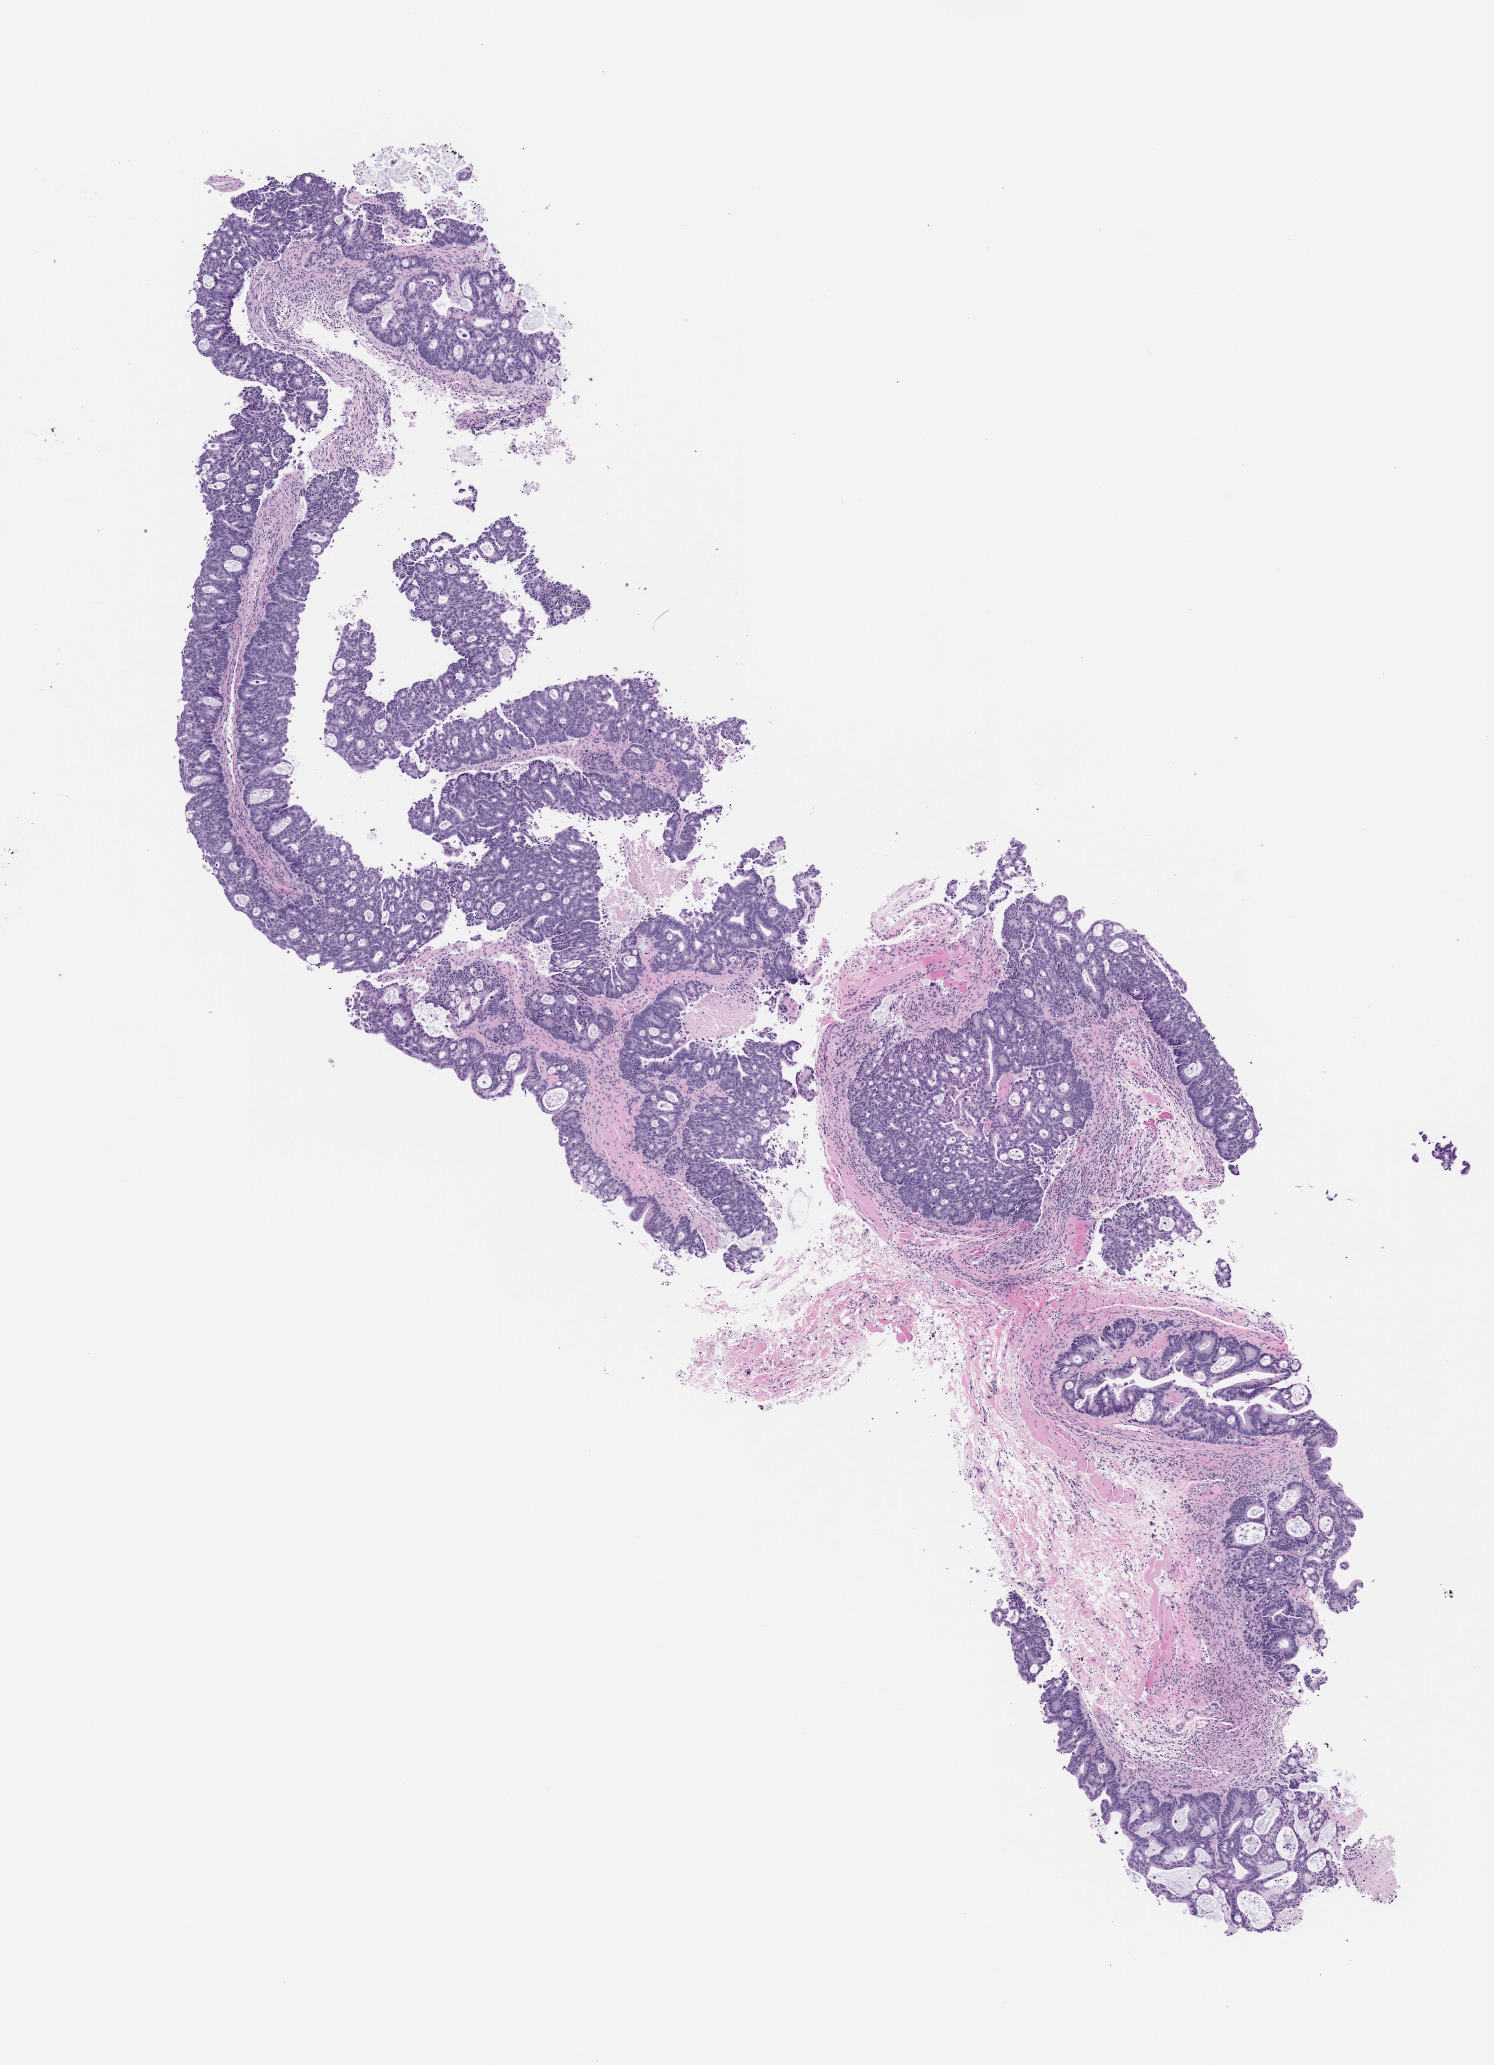
H&E whole-slide image of a patient-derived xenograft (PDX) tumor grown in a mouse, passage 1 — a low-resolution overview of the entire scanned area, about 6.0 x 8.3 mm, formalin-fixed paraffin-embedded section, originating tumor site category: colon.
Originating patient diagnosis: Colon Adenocarcinoma.